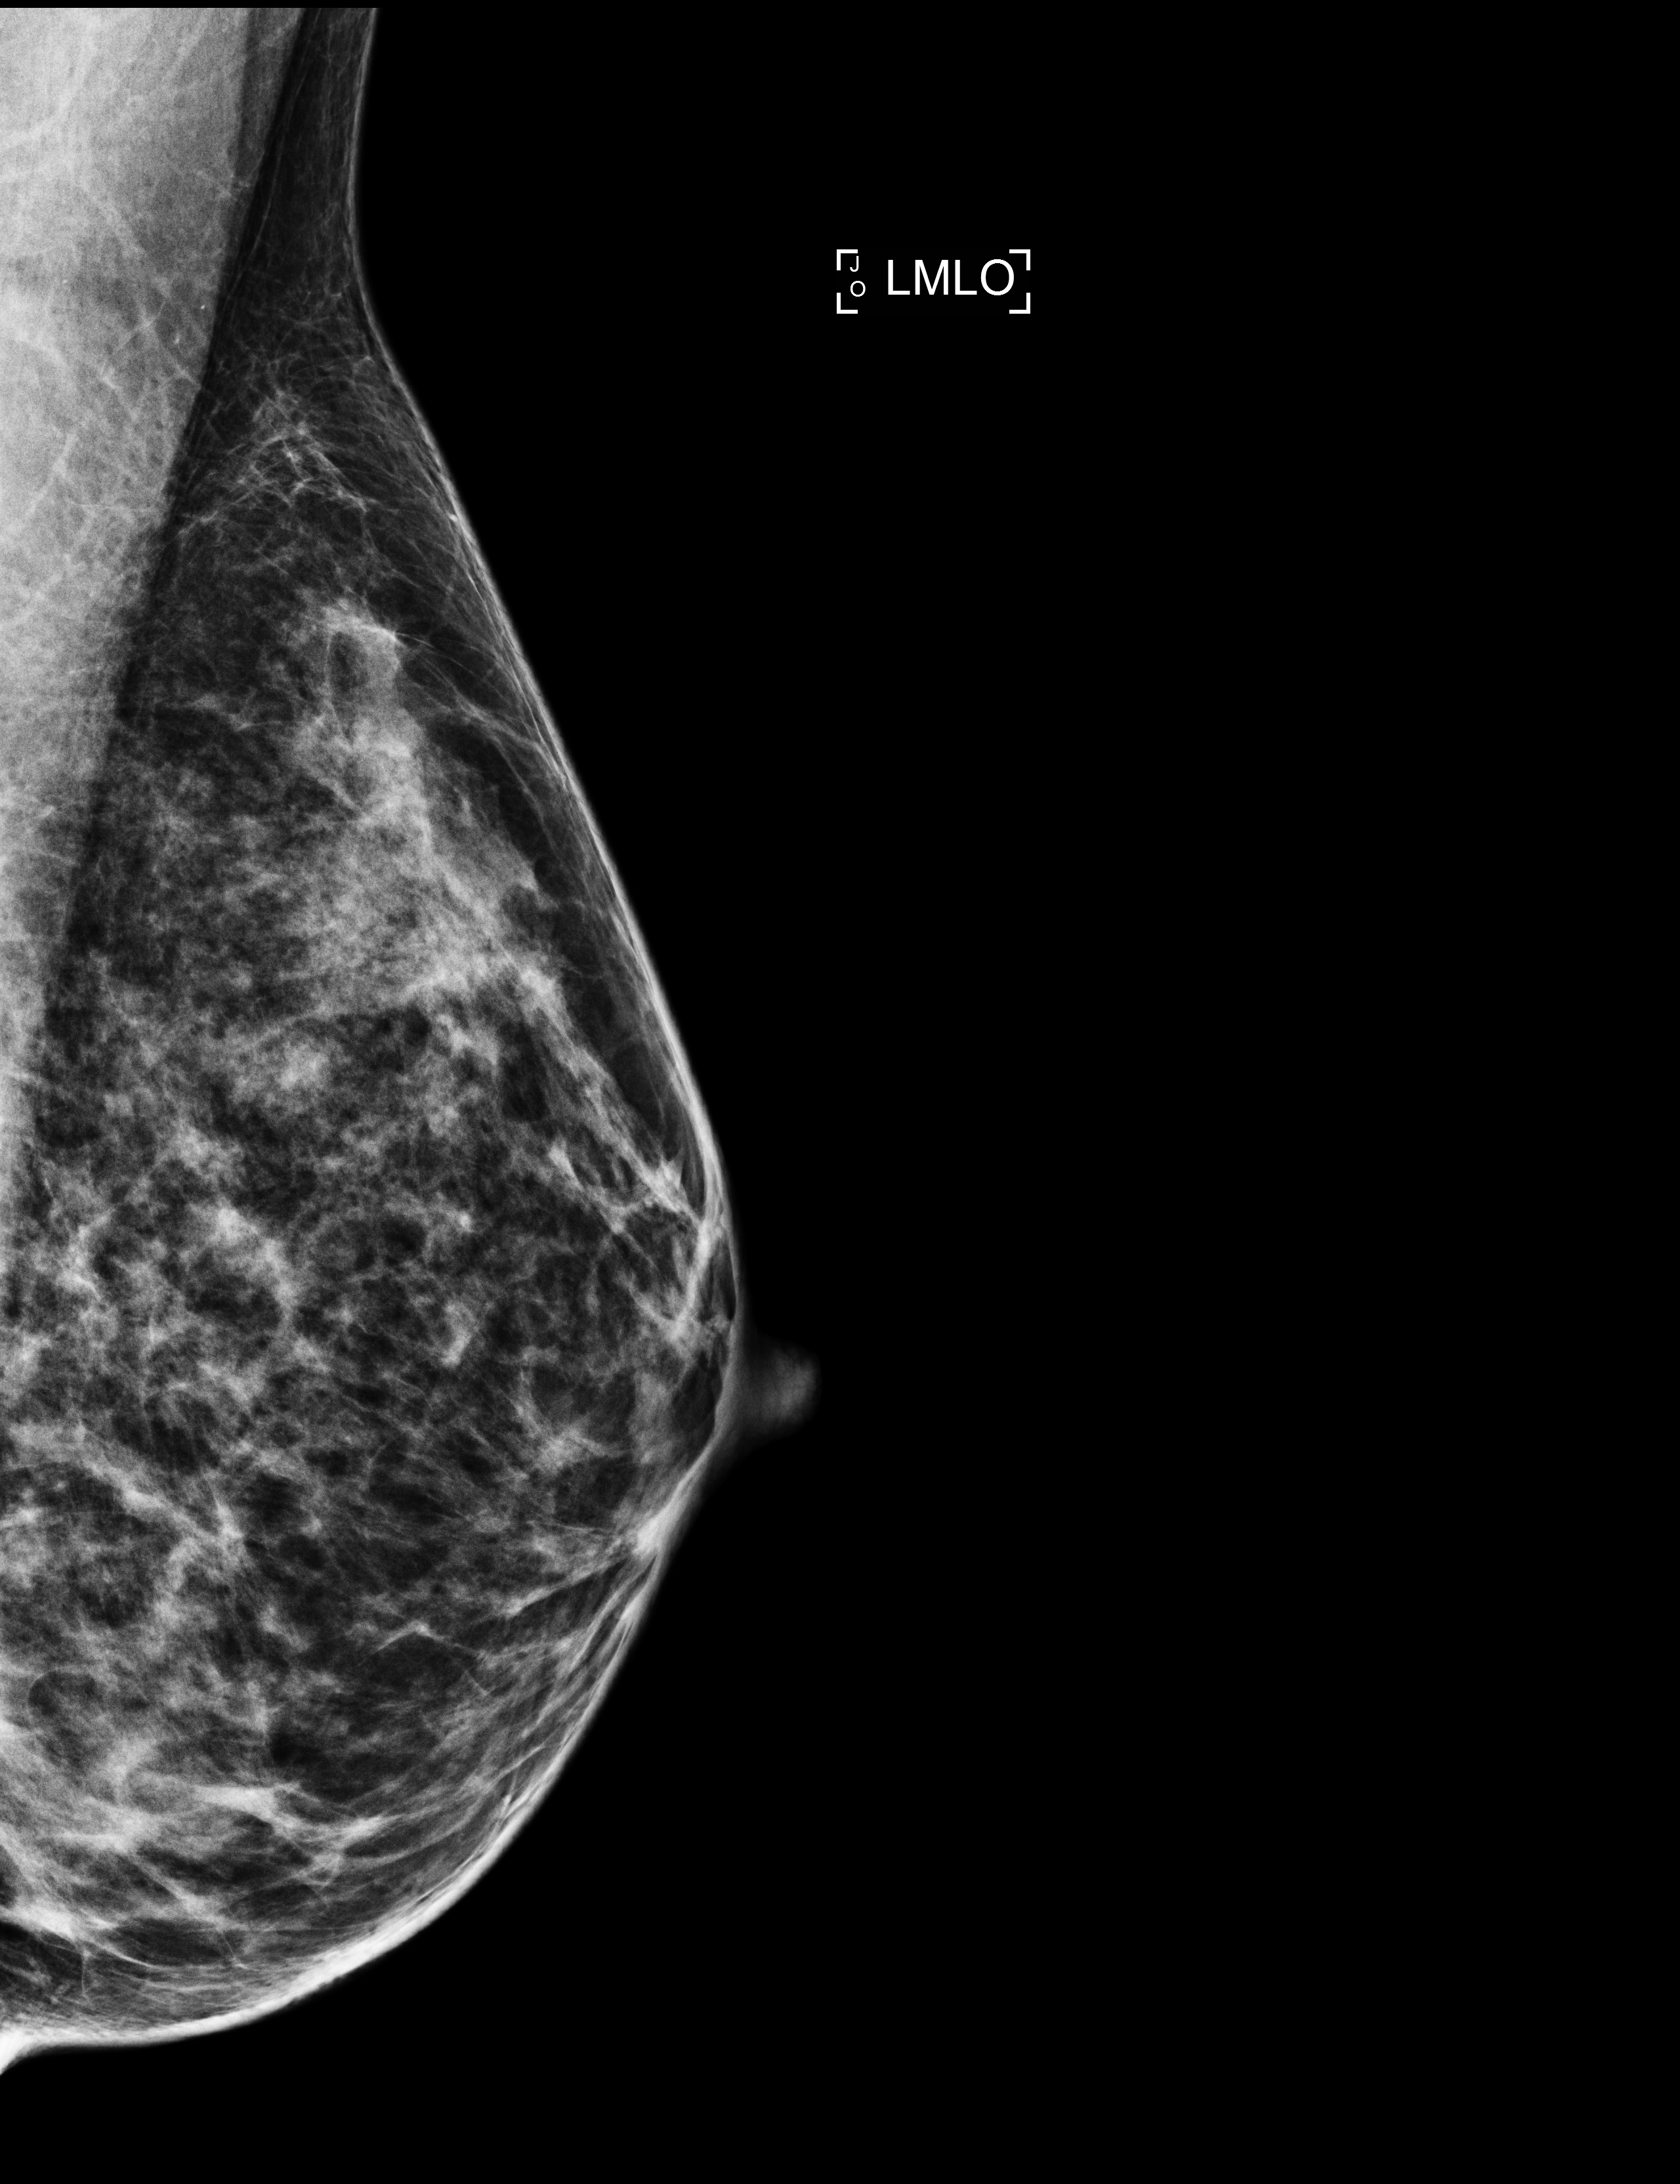
Screening examination, compressed breast thickness 46 mm, system: Selenia Dimensions. Patient aged 41 years (female).
Image type: full-field digital mammogram. Breast: left. Projection: mediolateral oblique (MLO) view. BI-RADS breast density category at the screening exam (both breasts, scale 1–4): 3. Final BI-RADS category for the screening round (tomosynthesis exam, both breasts): category 1. Recall: no recall after this screen.